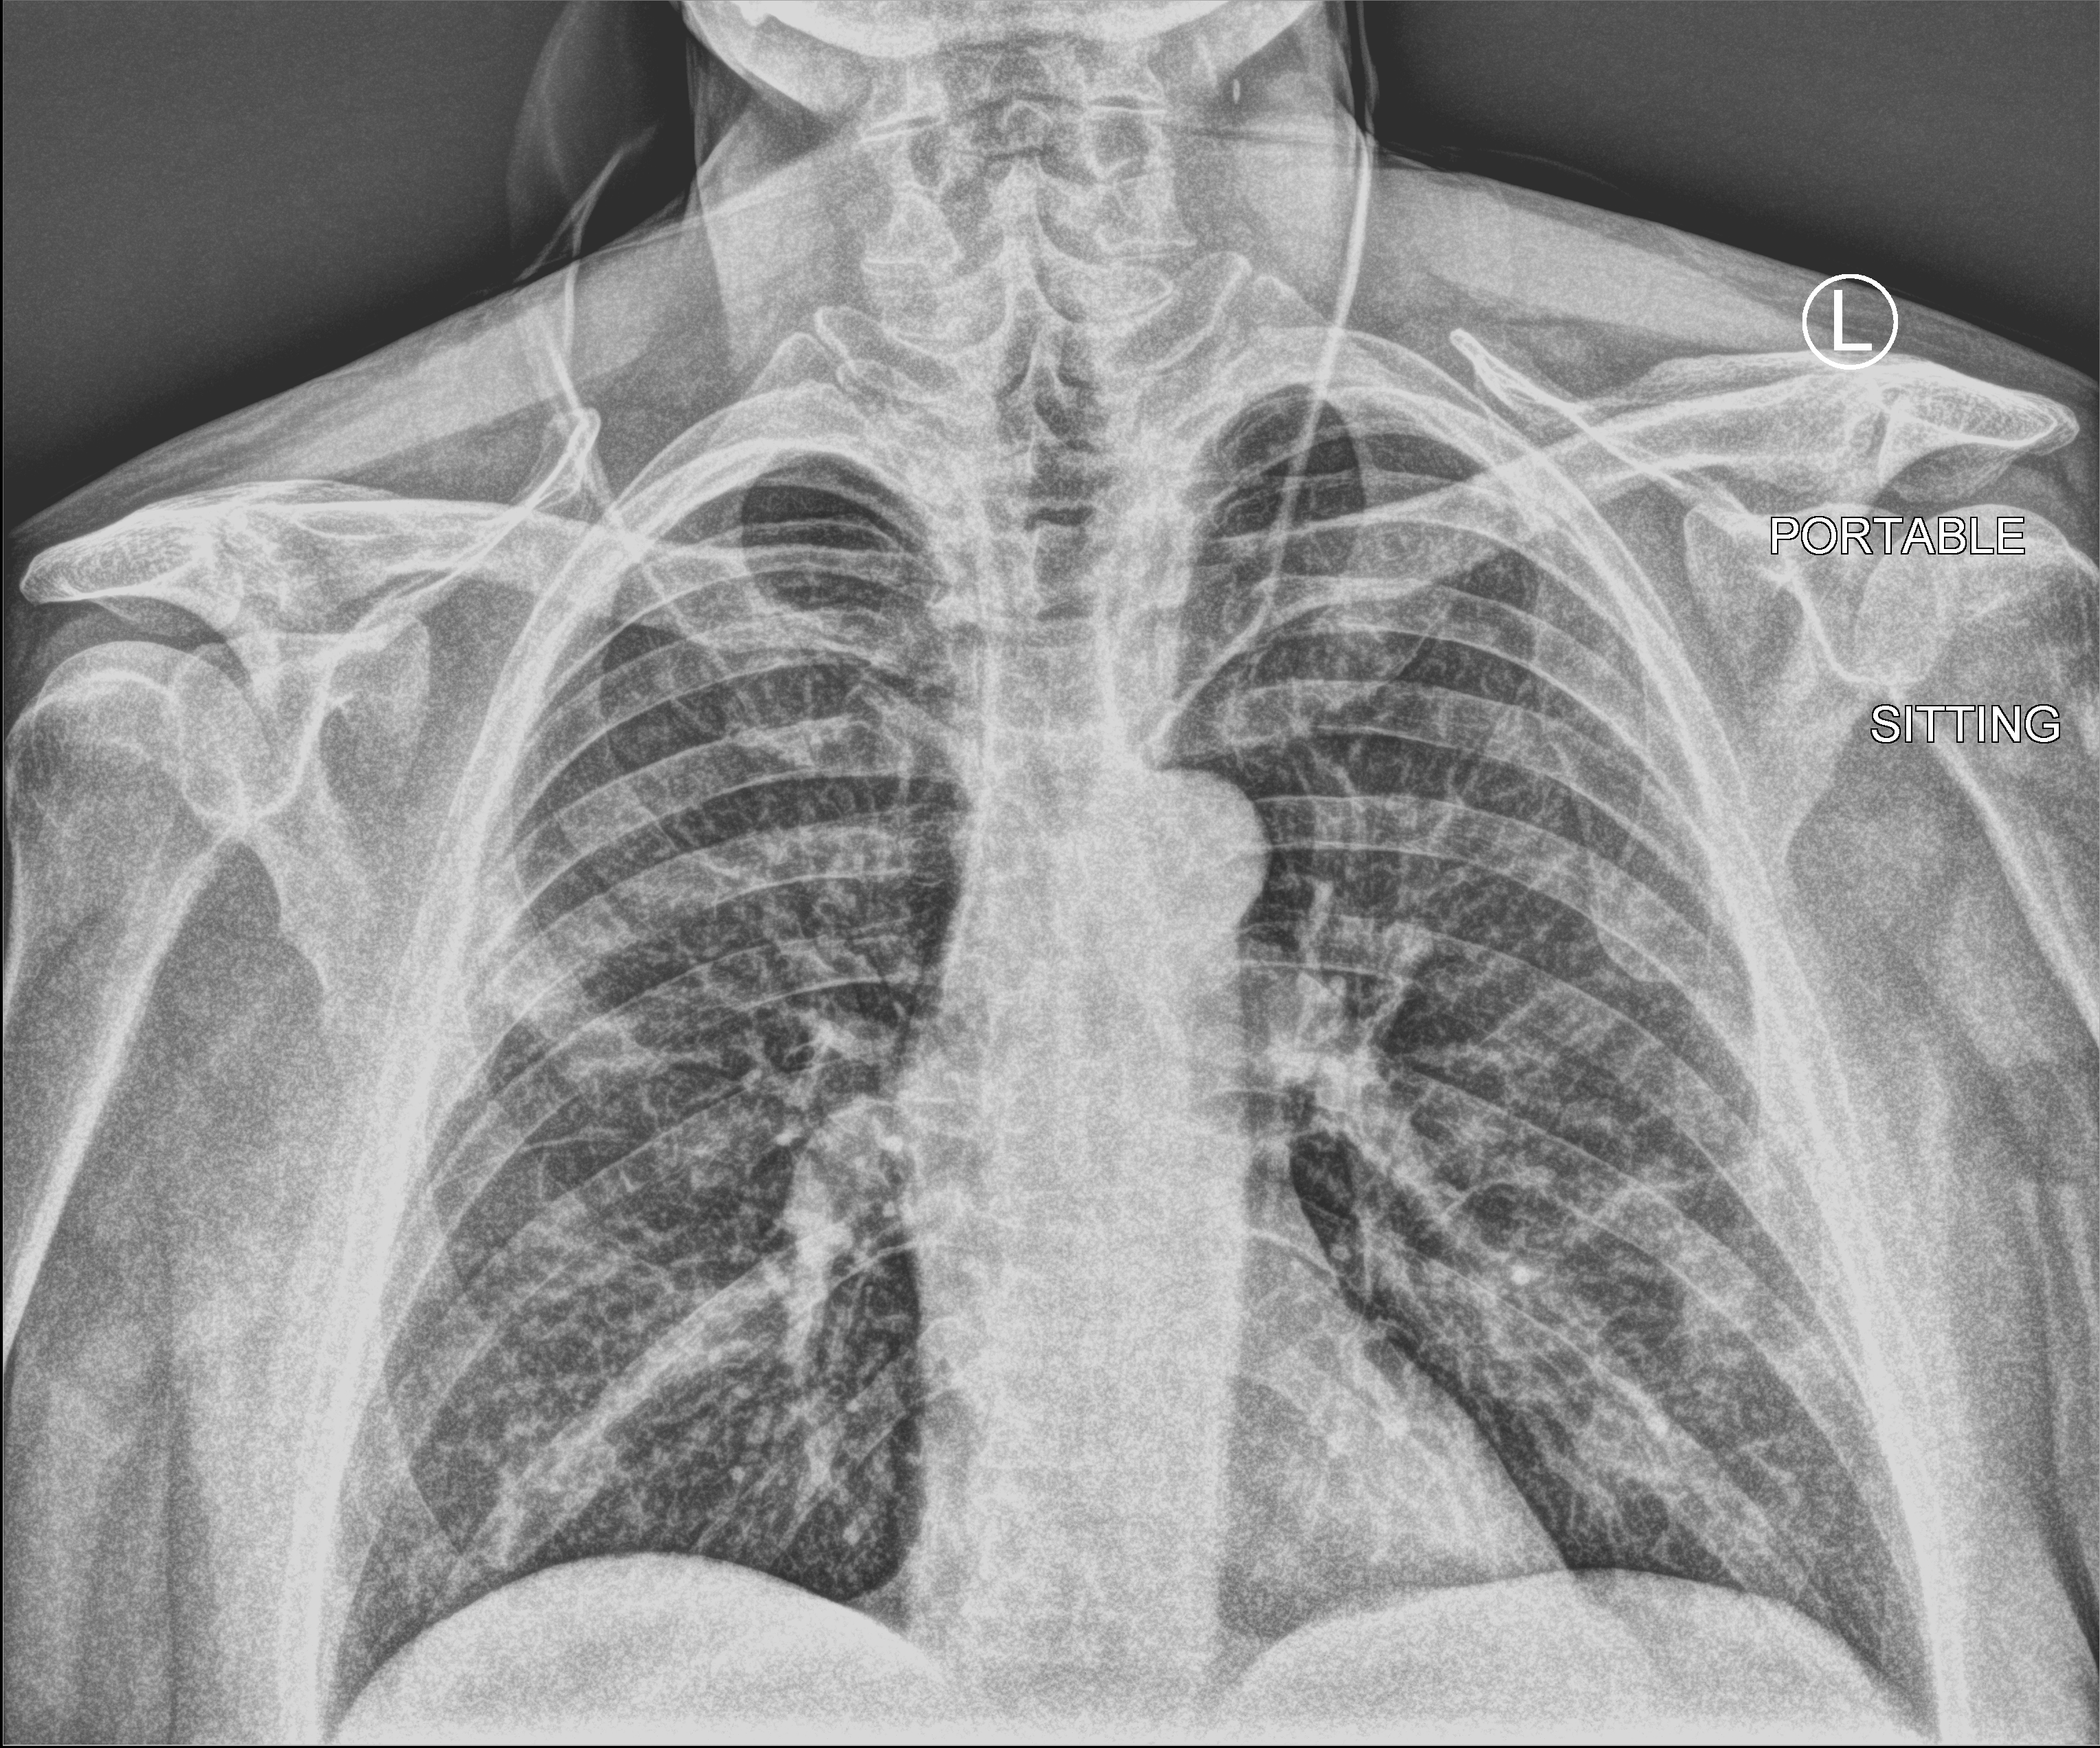
Portable chest radiograph, anteroposterior (AP) projection. Male patient hospitalised with COVID-19, age 60–74 years.
From the hospital-stay record, not from the radiograph (when in the stay this image was taken is not recorded):
- admitted to intensive care during this hospital stay: no
- hypertension (admission record): no
- mechanically ventilated during this hospital stay: no